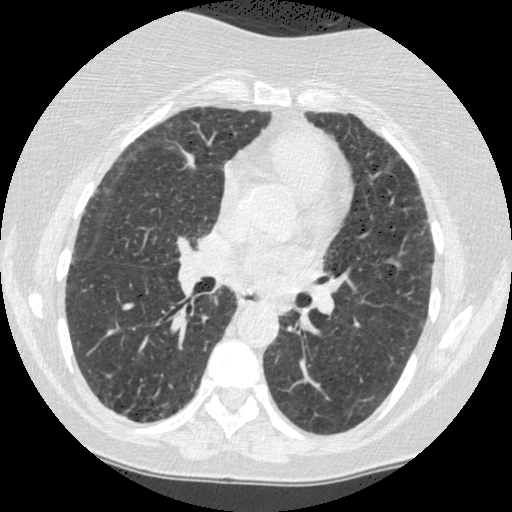
Low-dose screening chest CT, axial slice. Baseline annual screen. Lung window (W 1500 / L -600 HU). Slice 213 of 442 in the series. 512 × 512 image matrix, field of view 310 × 310 mm. Female, age 60 years at enrolment.
Lesion marked by an expert reader, bounding box <262,288,305,329> (left, top, right, bottom; pixels). The screening reader recorded 2 non-calcified nodules or masses ≥4 mm on this exam (right lower lobe, left lower lobe); which of them this box marks is not recorded. Official screen result: positive, change unspecified: nodule(s) >= 4 mm or enlarging nodule(s), mass(es), or other non-specific abnormalities suspicious for lung cancer. Lung cancer was diagnosed 794 days after this screen (after the third annual screen): small cell carcinoma, NOS, left lower lobe, undifferentiated (G4), stage IV (AJCC 6th edition), 69 mm at pathology.